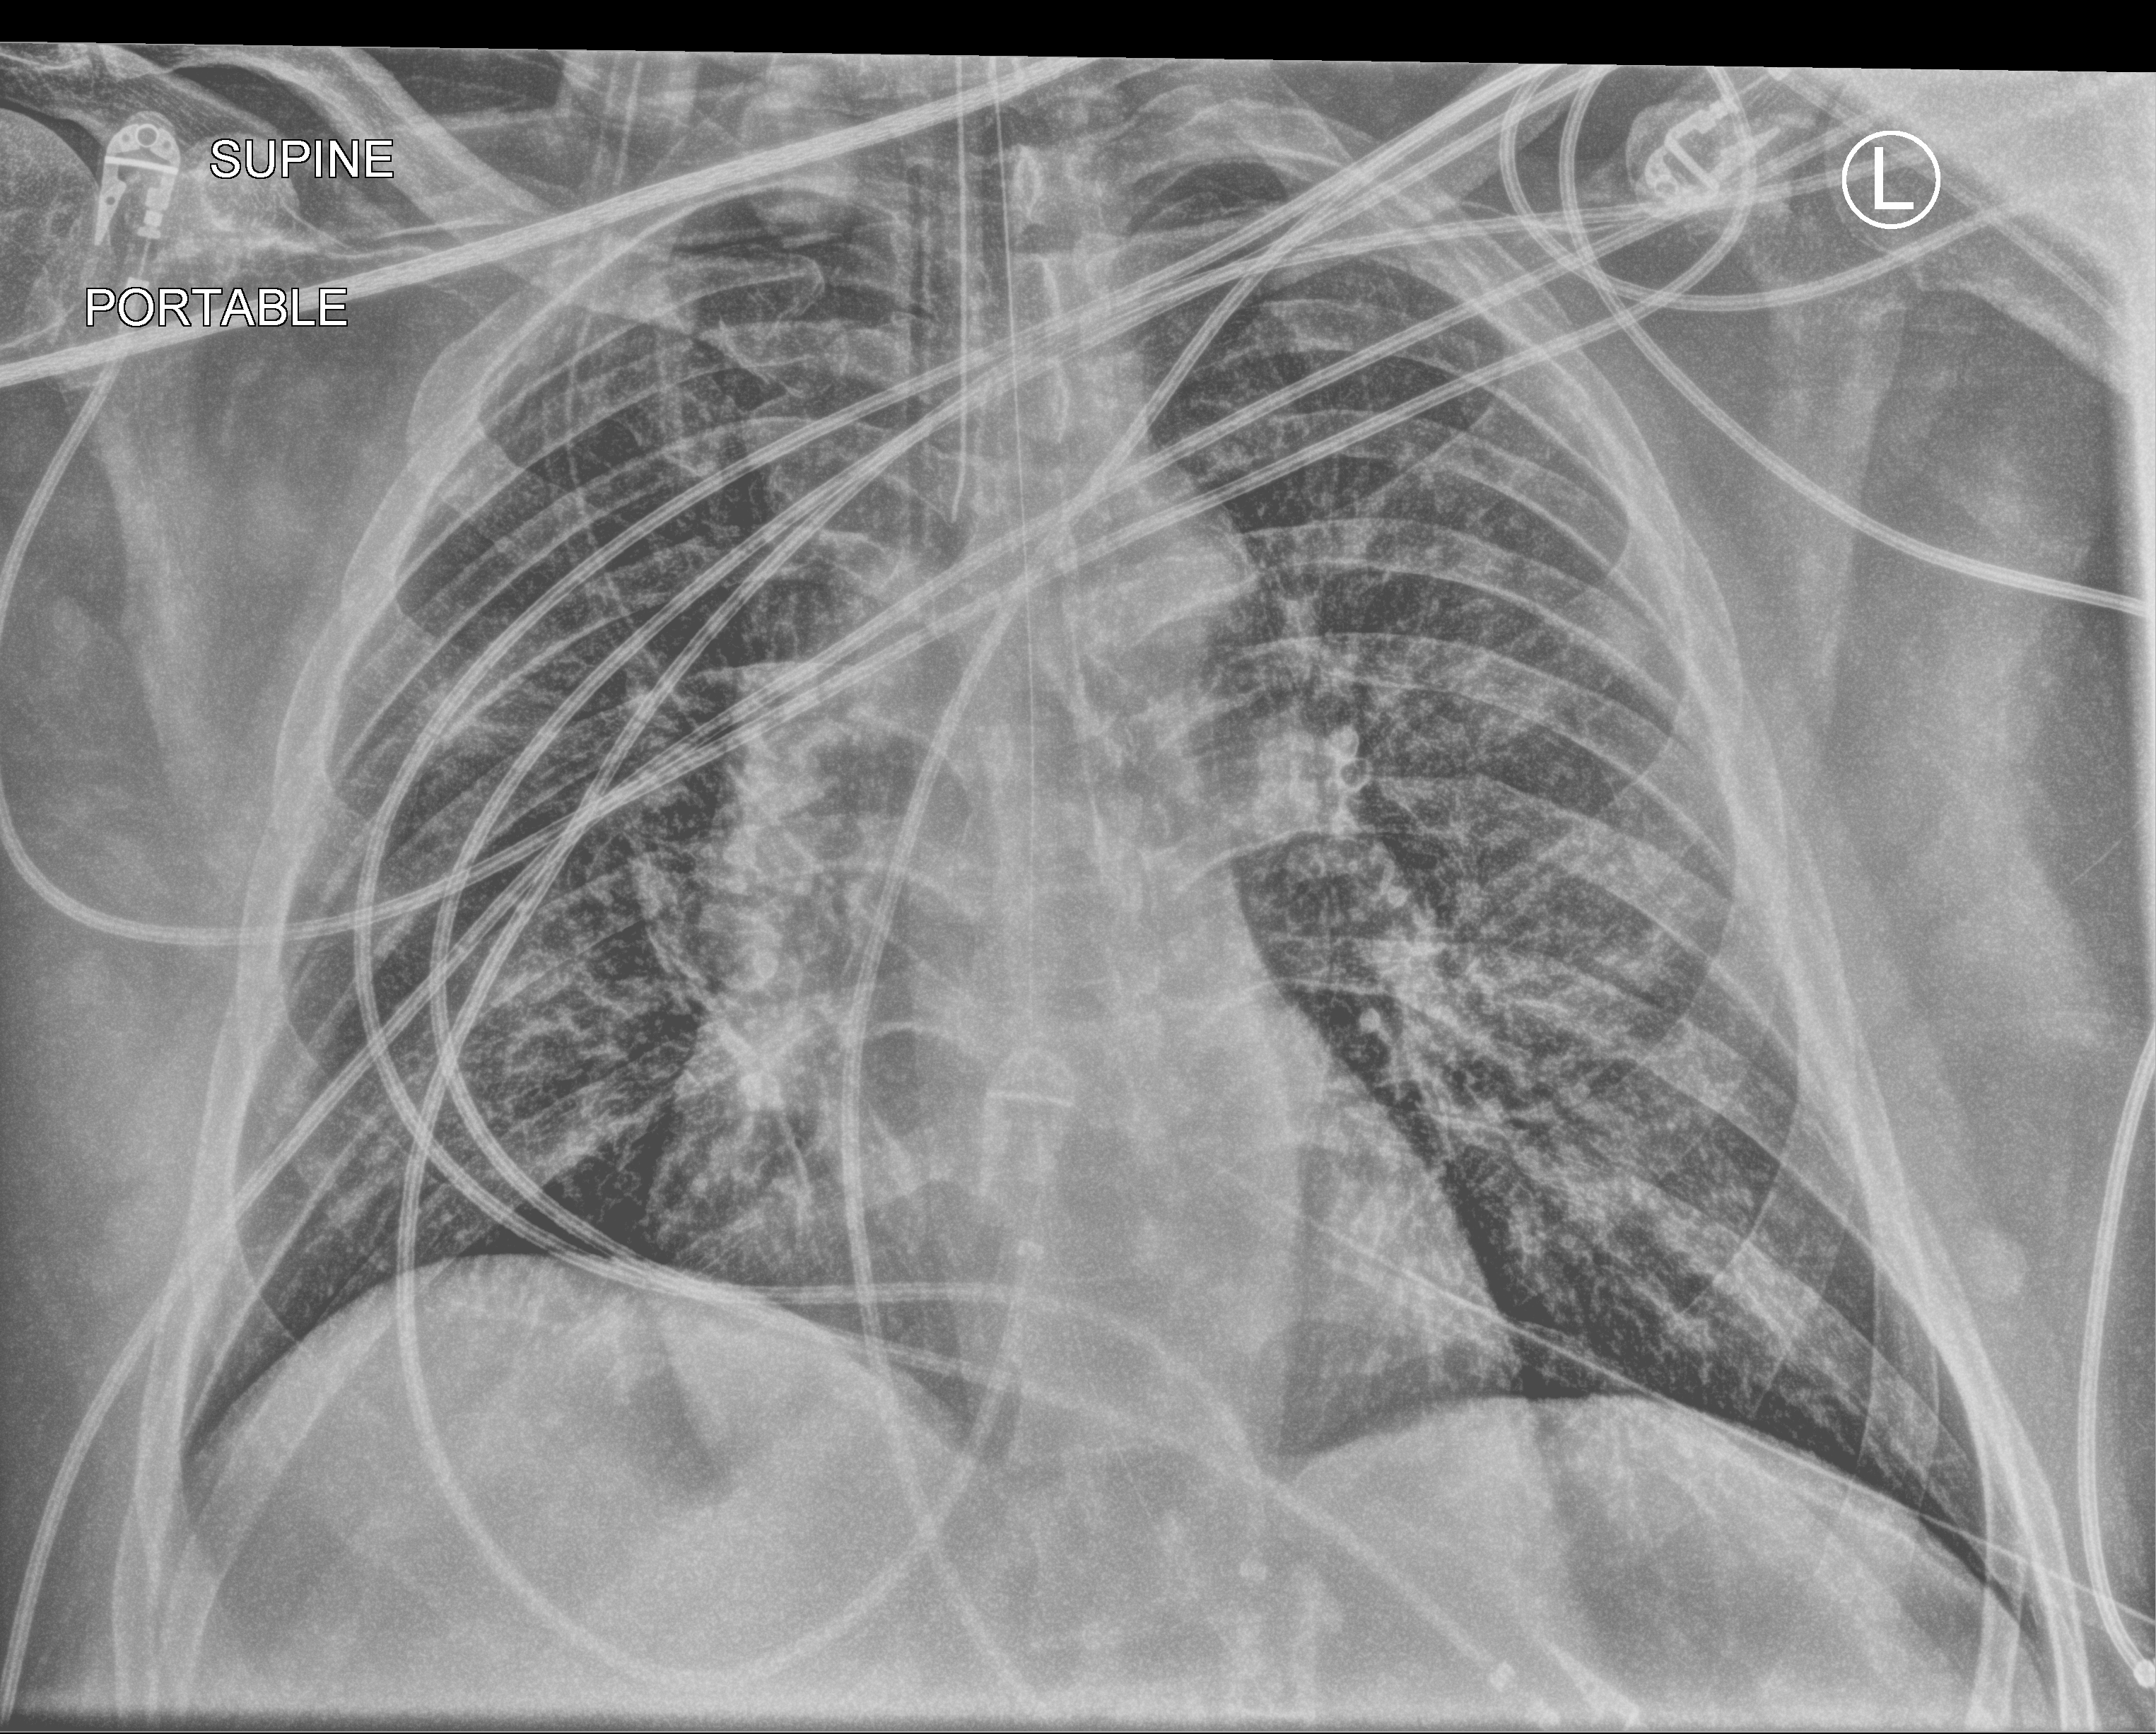
Portable chest radiograph; anteroposterior (AP) projection. Male patient hospitalised with COVID-19, age 60–74 years.
From the hospital-stay record, not from the radiograph (when in the stay this image was taken is not recorded): length of hospital stay: 17 days; diabetes (admission record): yes; admitted to intensive care during this hospital stay: yes.